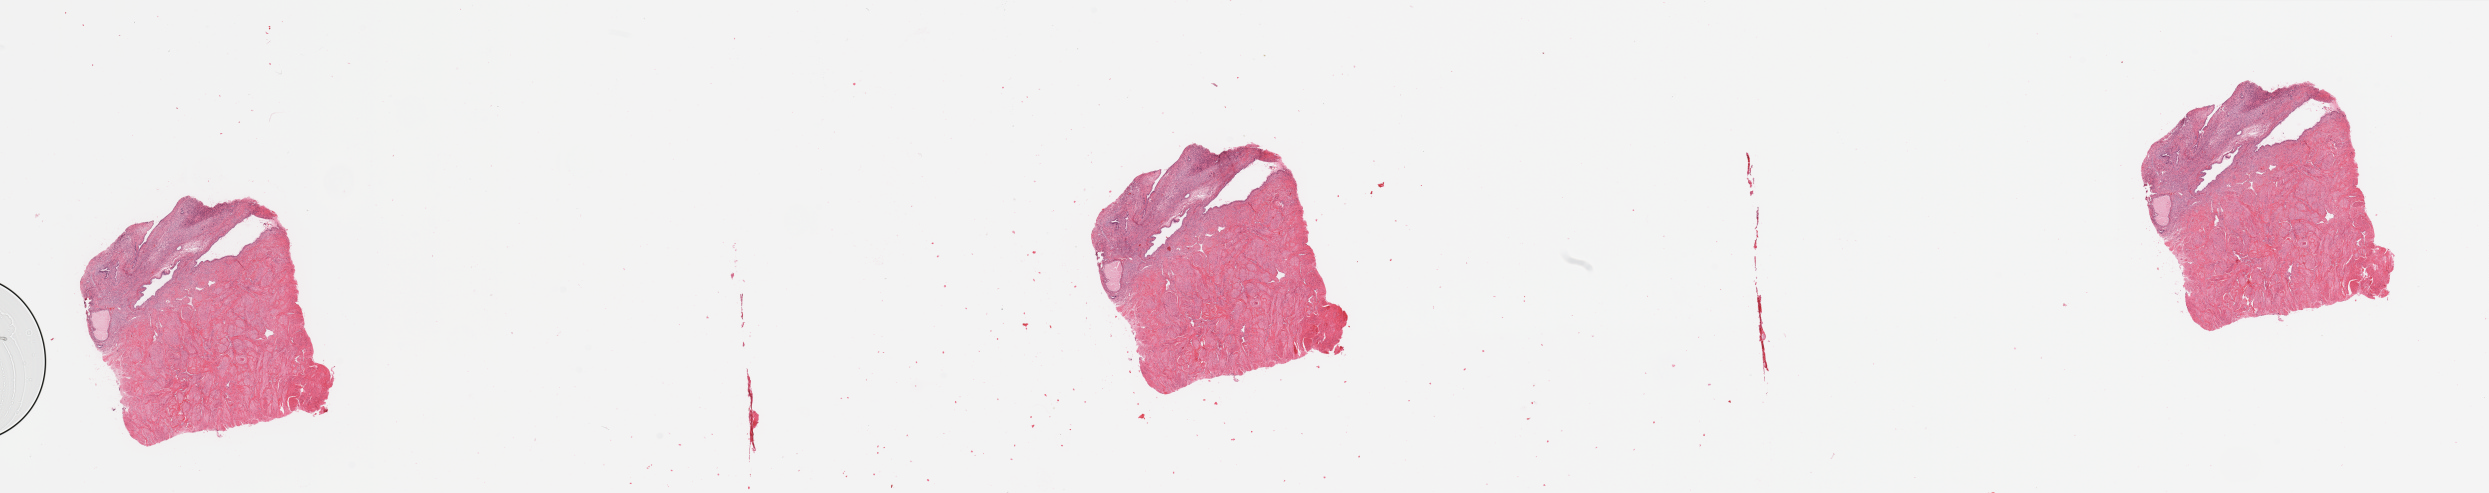
Whole-slide histology image, Hematoxylin and eosin (H&E) stained — whole scanned area (about 39.4 x 7.8 mm, from a 20x scan) shown as a low-resolution overview, uterus, normal (non-tumour) tissue. Female, 56 y/o.
This section: normal (non-tumour) tissue from the same patient. Patient diagnosis: Endometrioid adenocarcinoma, NOS.